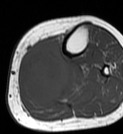
MRI of an extremity soft-tissue mass, one axial slice; position 27 of 68 along the scan axis; MR volume resampled by the dataset authors to the PET/CT grid (not the native acquisition matrix); 123 × 134 image matrix, field of view 120 × 131 mm. Female patient. From the clinical record (not read from this slice): histological type: extraskeletal high grade osteogenic sarcoma; grade: high; site of the primary tumour: left calf.
Annotated regions visible in this slice (expert contour drawn on MRI and transferred to this co-registered scan by the dataset authors):
- gross tumour volume (mass): bounding box [x1, y1, x2, y2] px = [19, 39, 69, 104]